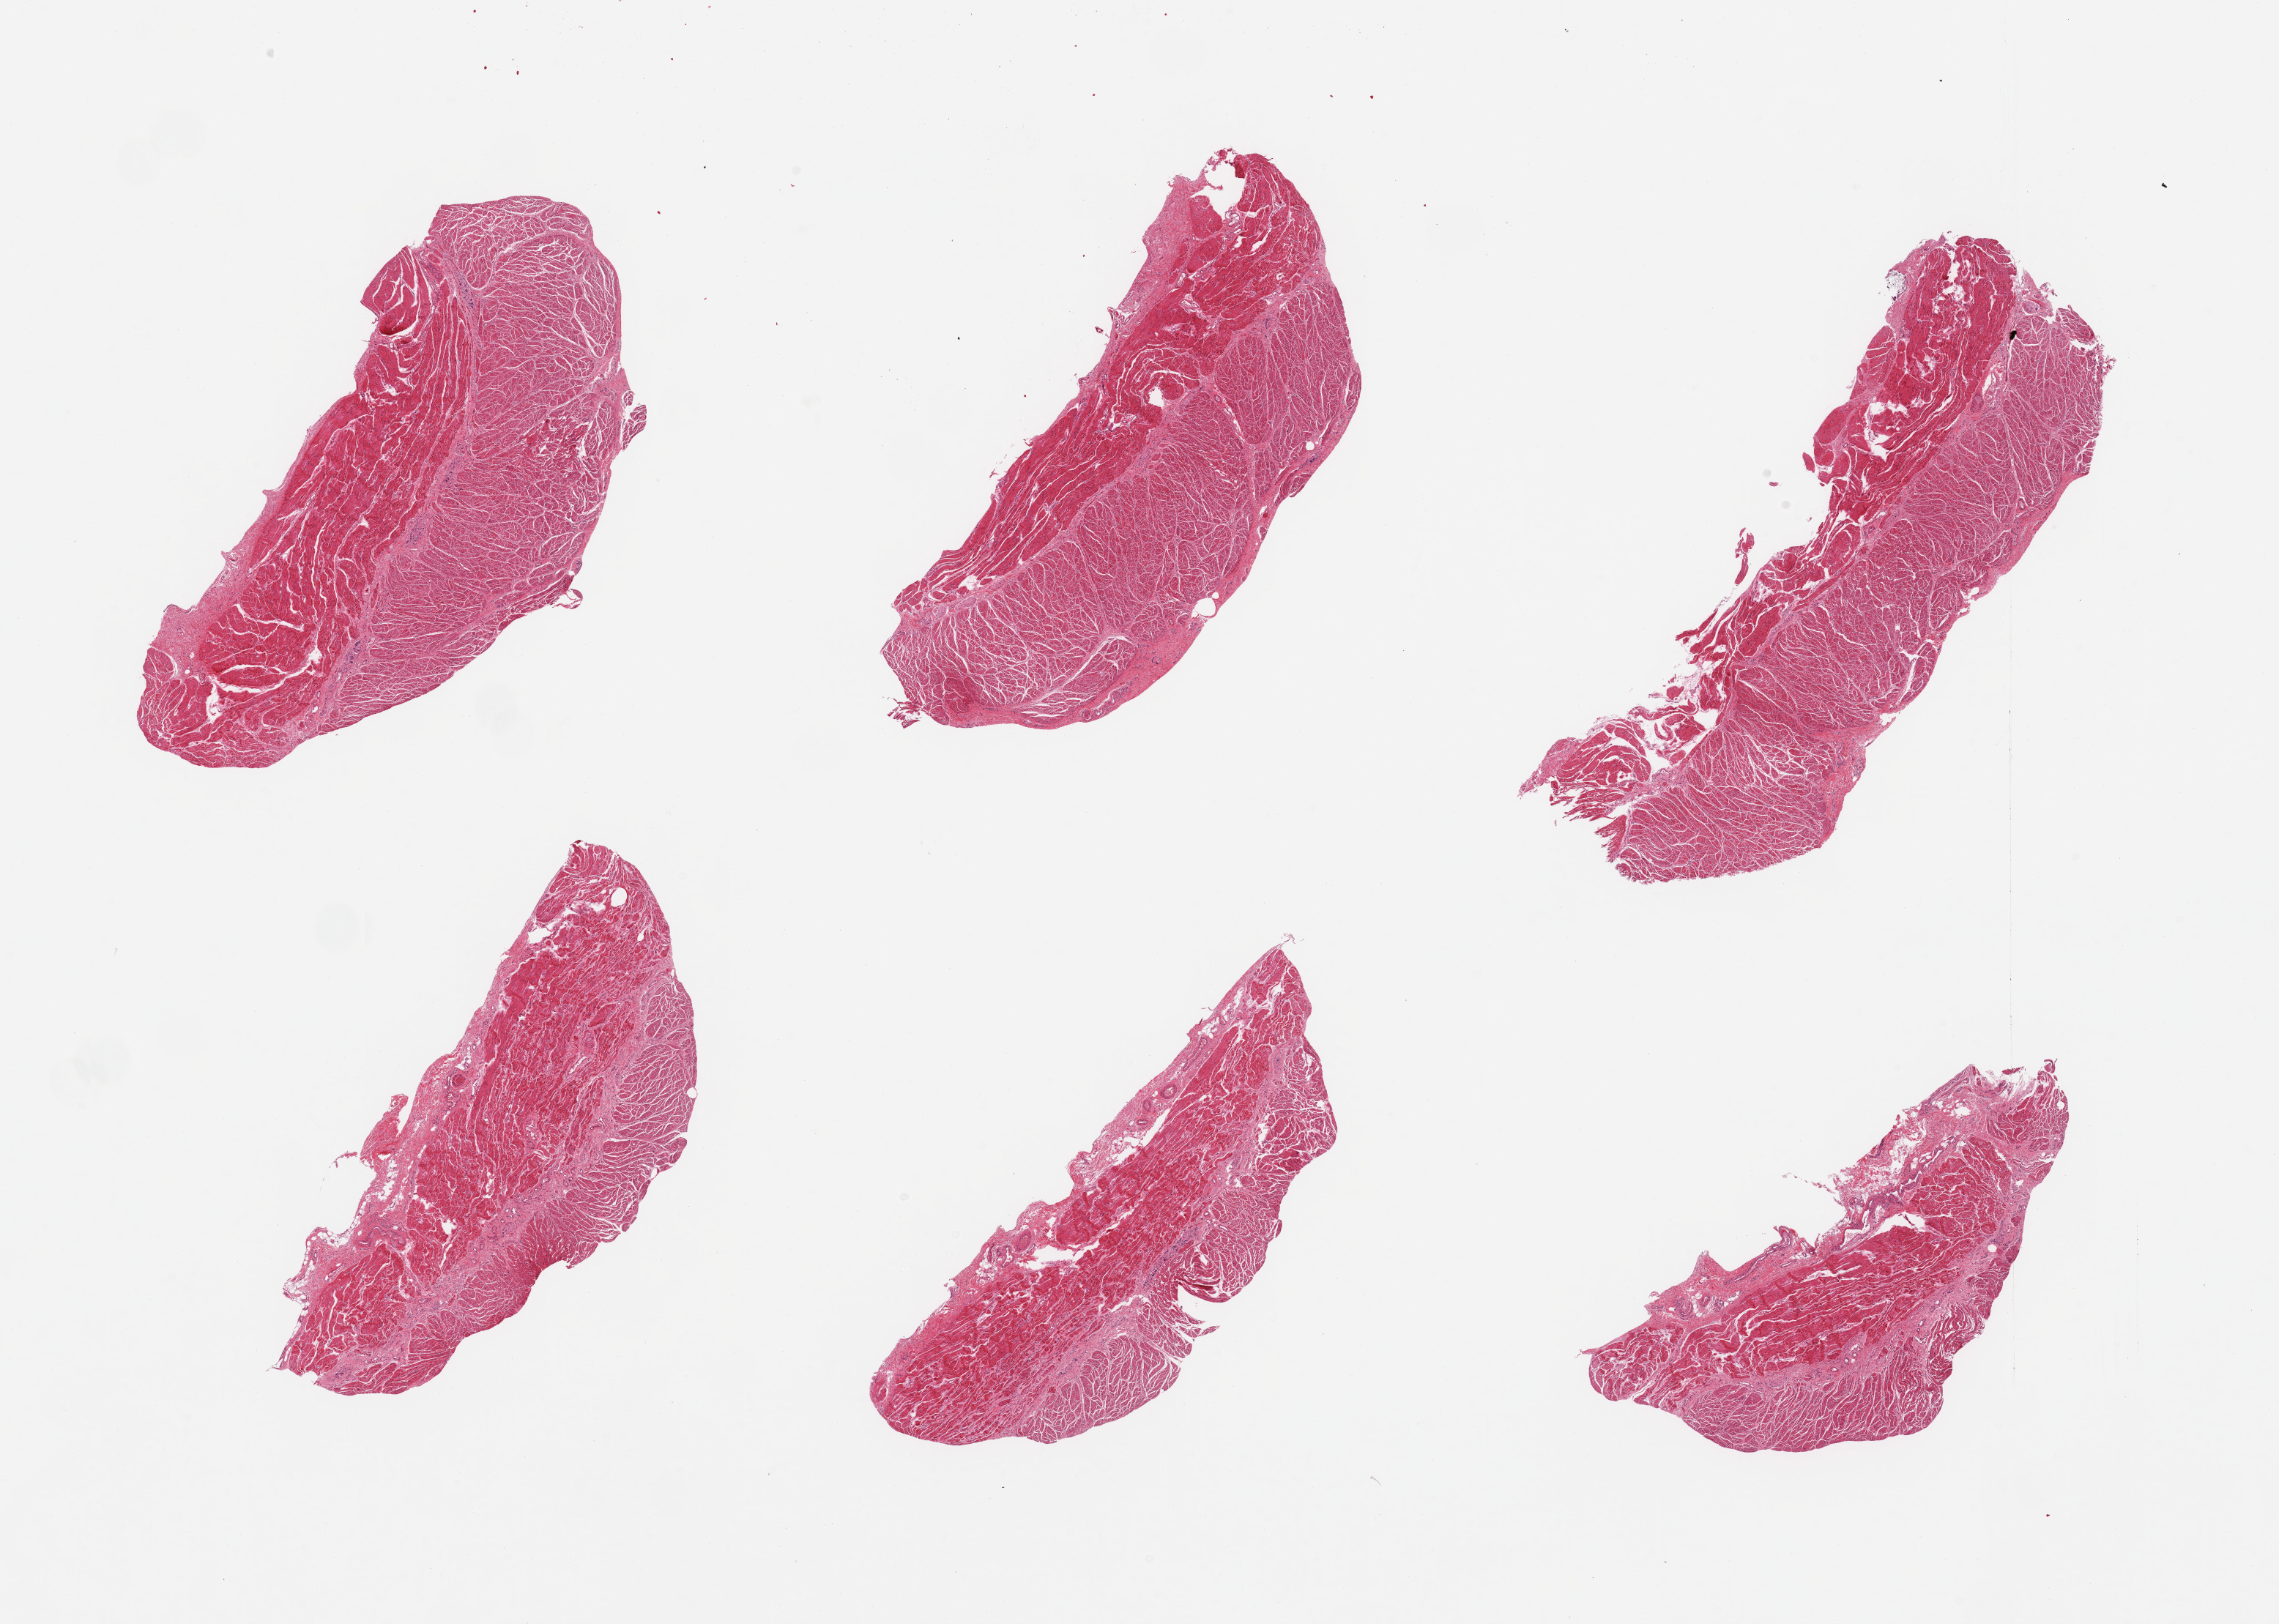
Whole-slide image, H&E stain, brightfield, a low-resolution overview of the entire scanned area, about 24.6 x 17.5 mm; PAXgene-fixed, paraffin-embedded tissue; section of gastroesophageal junction (target tissue); donor tissue sample. Donor sex: male.
• review note (as recorded): 6 pieces, confirmed target muscularis